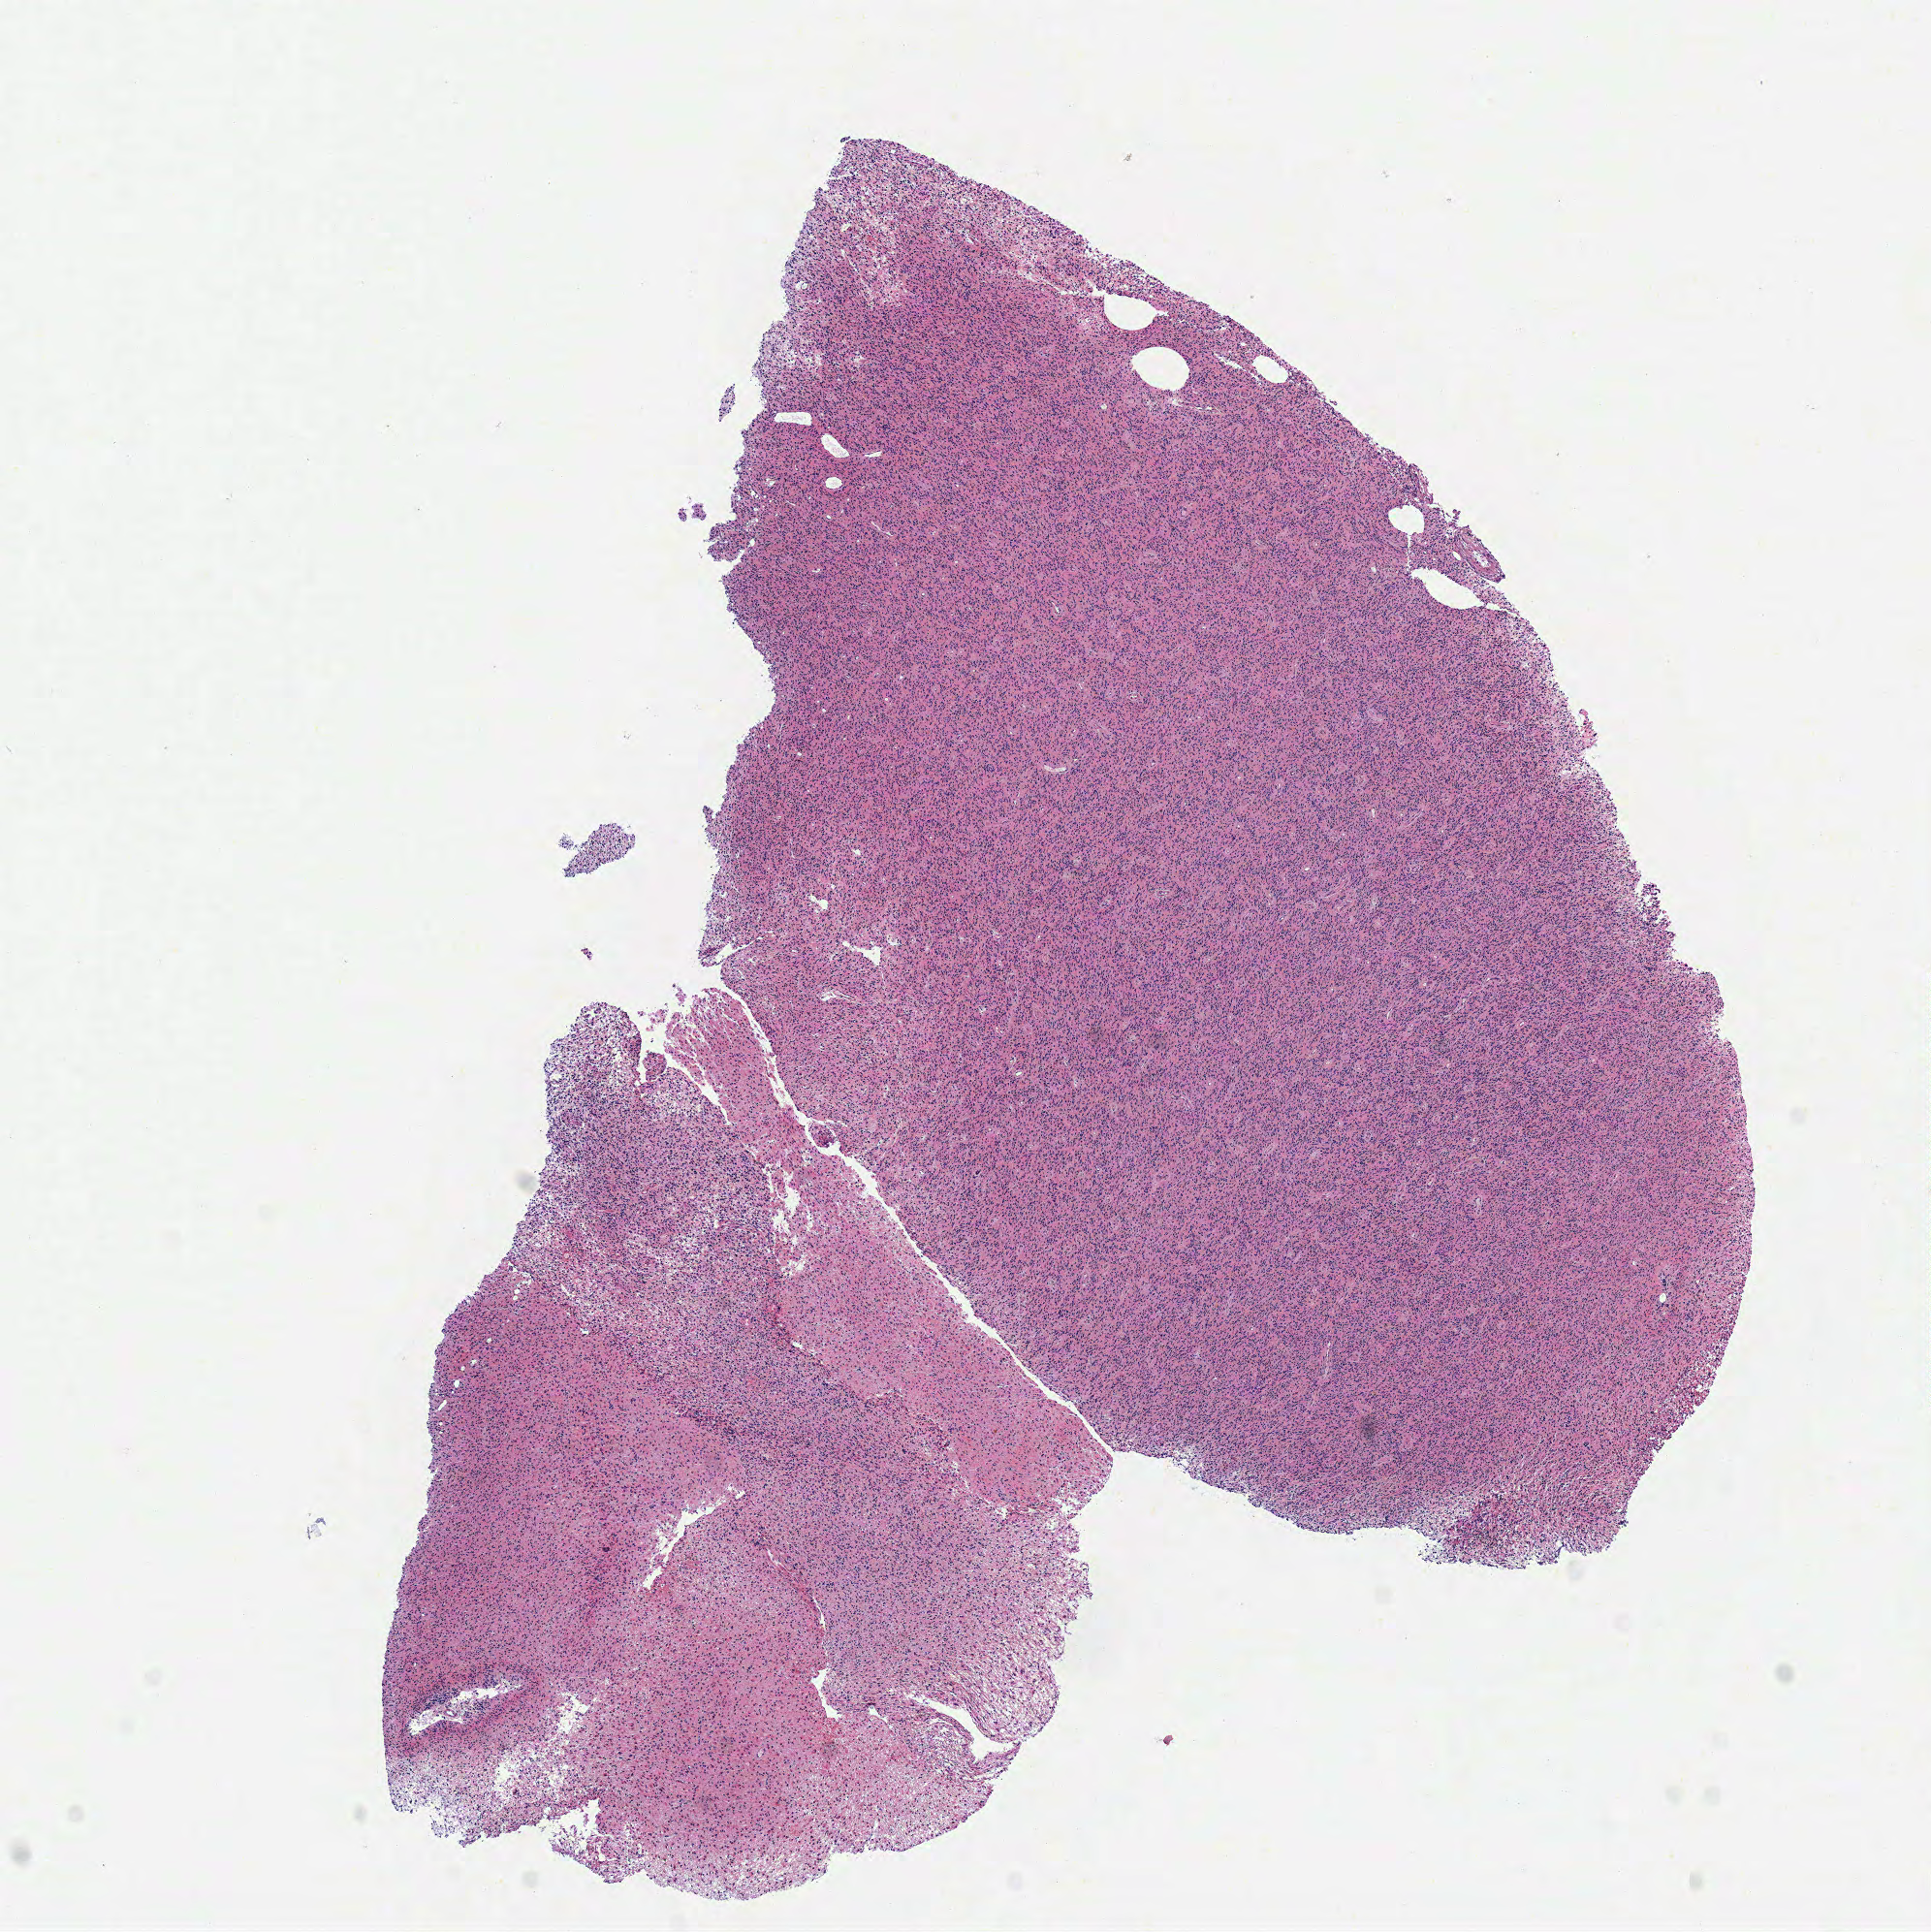
Digitized H&E-stained tissue section (whole slide) — shown as a low-resolution overview of the whole scanned area (about 7.8 x 7.8 mm, from a 40x scan); frozen section from the top of the tissue portion; sample: primary tumour, brain. Patient: female, age at initial diagnosis 51 years. Histologic grade: G3 (poorly differentiated). Slide review estimates, as recorded: tumour cells 100%, tumour nuclei 80%, normal cells 0%, stromal cells 0%, necrosis 0%.
• histologic diagnosis: Astrocytoma, anaplastic
• laterality: right